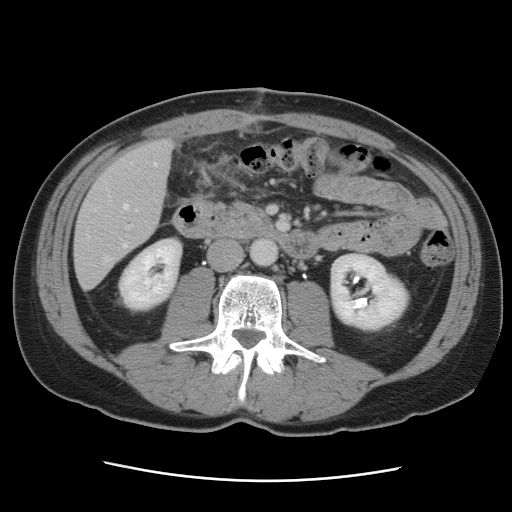
Contrast-enhanced abdominal CT, one axial slice. Position 25 of 89 along the scan axis. 120 kVp. Intravenous contrast given. Soft-tissue window (W 400 / L 40 HU). 5 mm slice thickness. 512 × 512 image matrix, field of view 366 × 366 mm. Male patient, age 59 years. From the clinical record (not read from this slice): diagnosis: colorectal cancer liver metastases, imaged before liver resection; multiple liver metastases: yes; largest metastasis: 0.6 cm.
Annotated regions visible in this slice (outlined manually by an expert reader):
- hepatic veins: bounding box [x1, y1, x2, y2] px = [88, 163, 157, 261]
- liver: [75, 141, 173, 288]
- planned liver remnant (the part of the liver to remain after resection): [76, 142, 173, 248]
- portal vein (with intrahepatic branches): [127, 225, 132, 229]